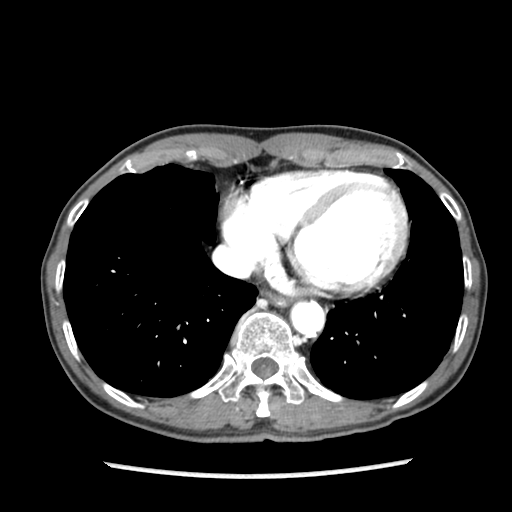
Contrast-enhanced abdominal CT (liver protocol), one axial slice; soft-tissue window (W 400 / L 40 HU); 2.5 mm slice thickness; 512 × 512 image matrix, field of view 300 × 300 mm. Case-level facts recorded for this patient, not image findings: diagnosis: hepatocellular carcinoma (patient treated with transarterial chemoembolisation; whether this scan precedes or follows treatment is not stated here); TNM stage (as recorded): Stage-IIIB; Child-Pugh class: A; tumour differentiation: well differentiated; tumour nodularity: uninodular.
Structures marked on this image (semi-automatic segmentation, software-assisted and operator-edited):
- abdominal aorta: bounding box (x1, y1, x2, y2) in pixels: (292, 302, 322, 335)